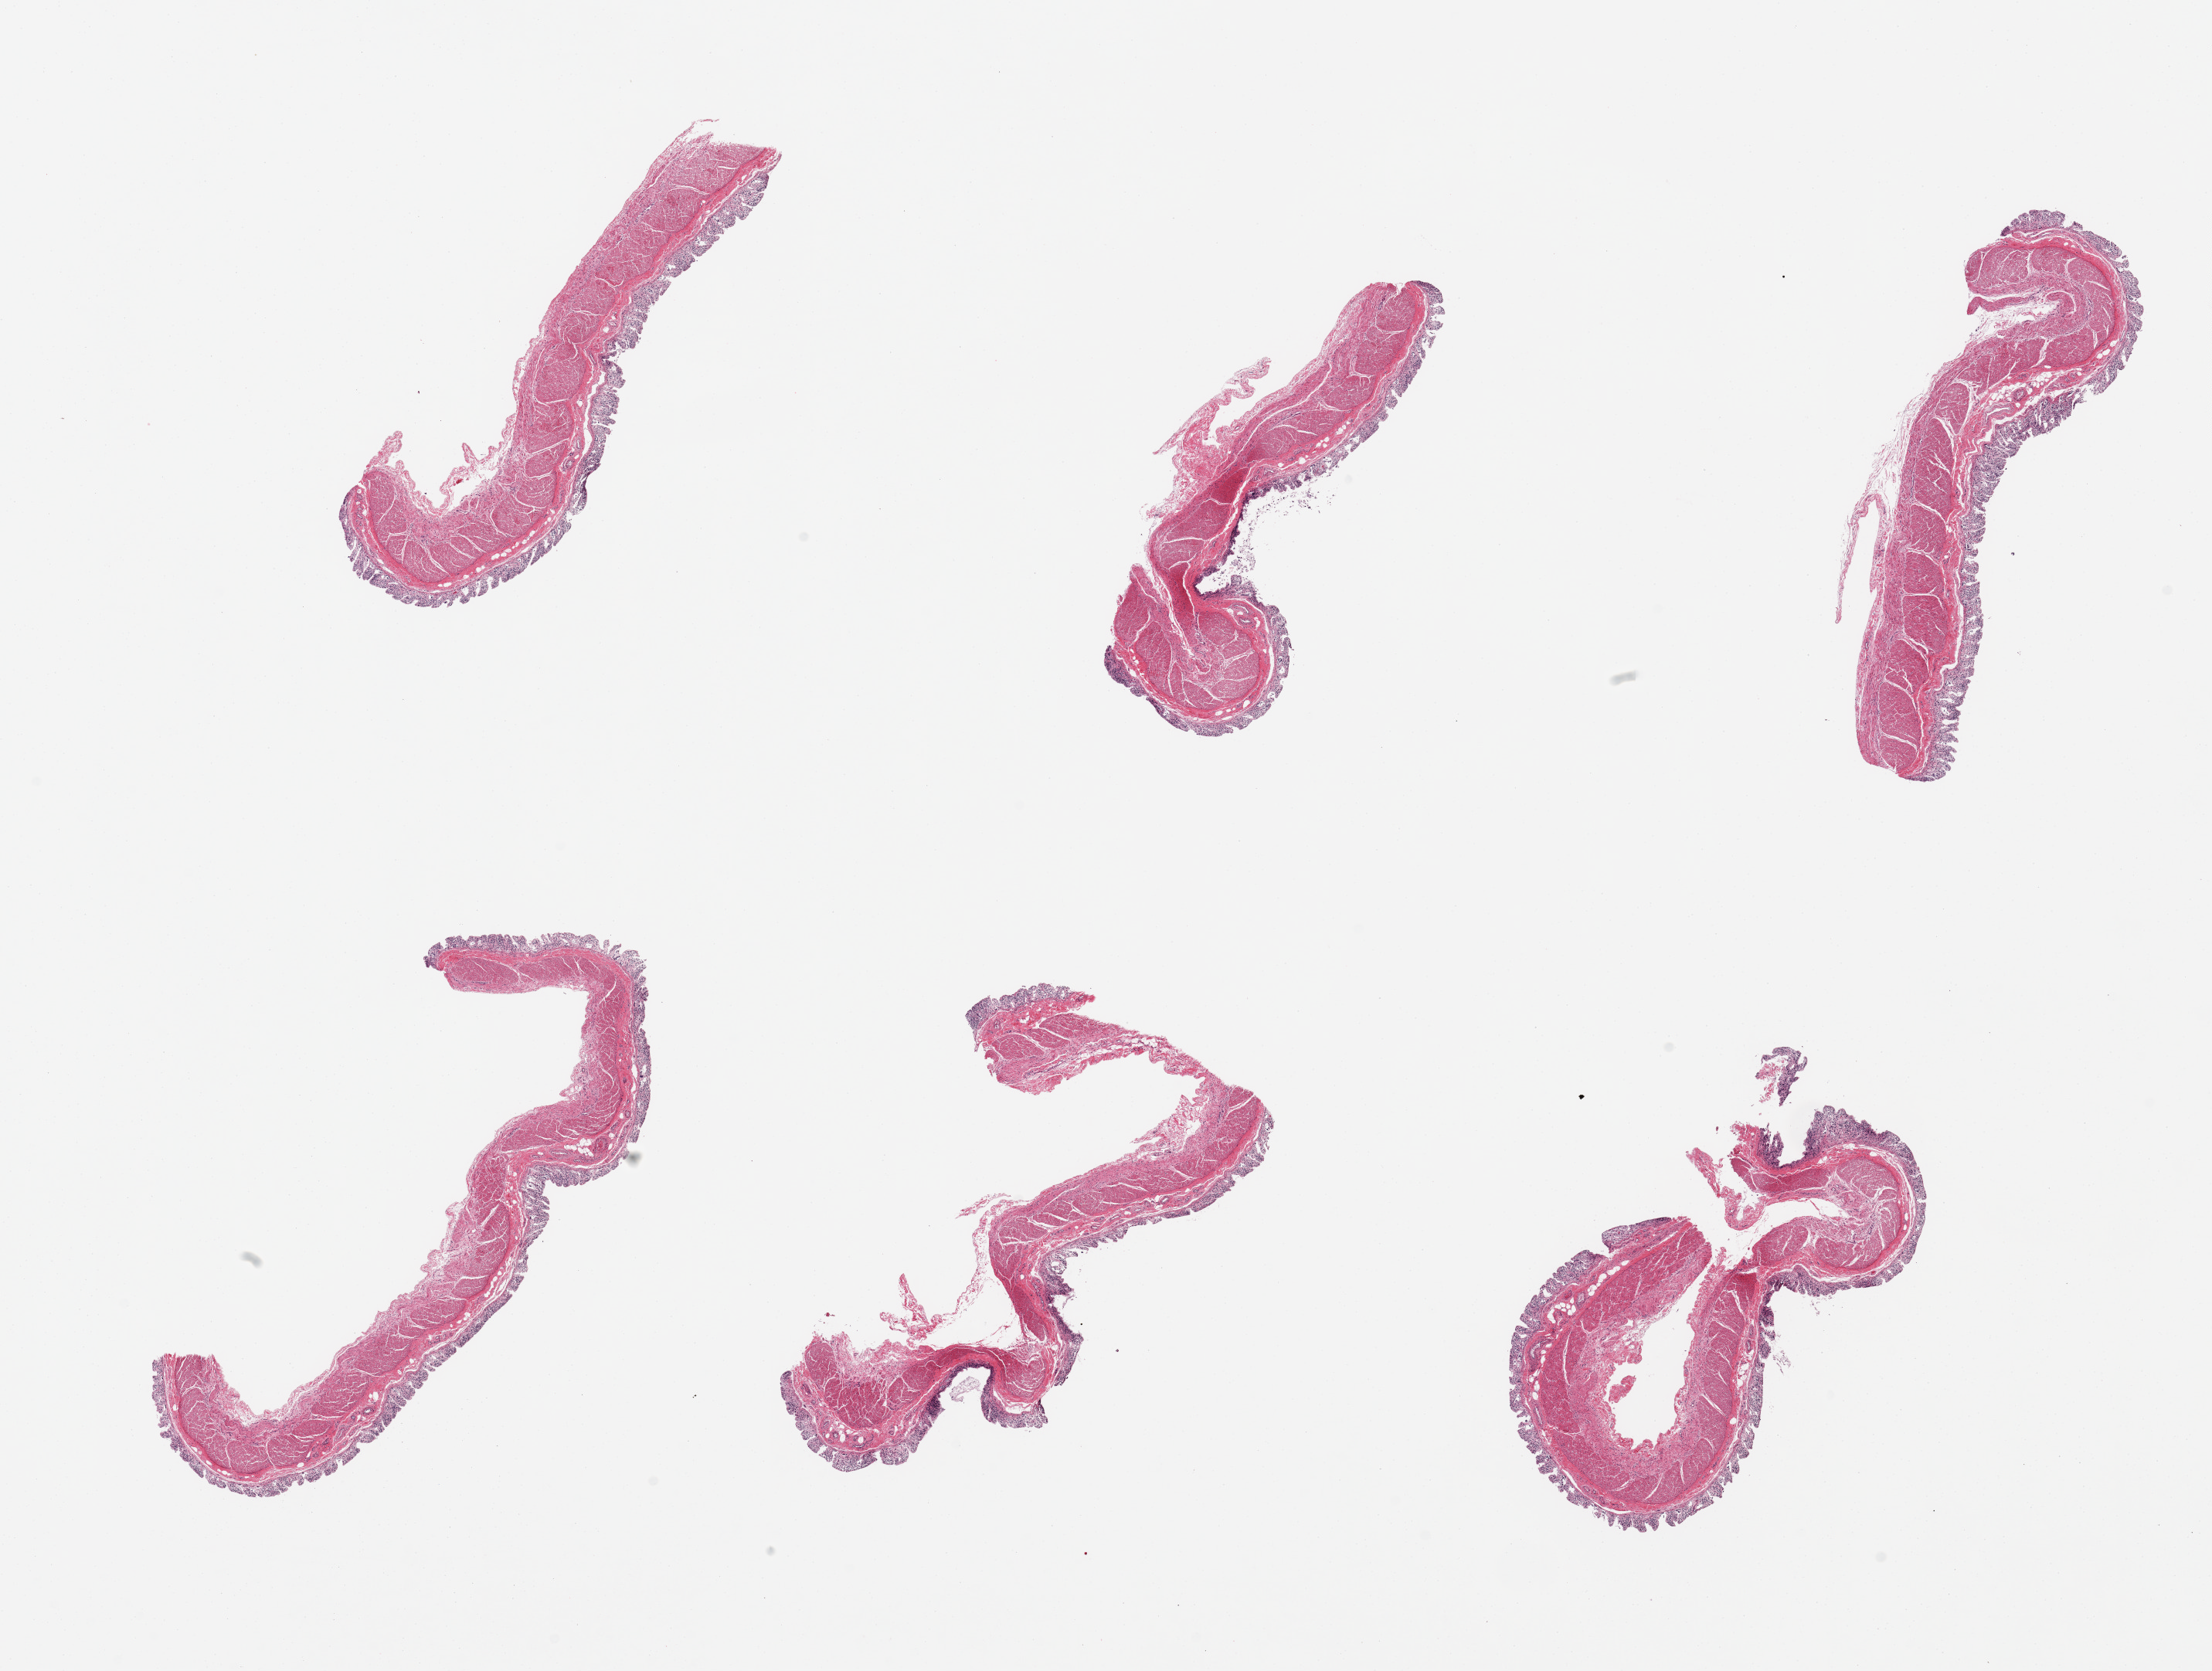
Whole-slide image, haematoxylin and eosin stain, low-resolution overview of the scanned area, about 22.6 x 17.1 mm (acquisition: 20x scan). PAXgene-fixed, paraffin-embedded tissue. Sampled site (target tissue): transverse colon. Donor tissue sample. Donor: male.
Review note (as recorded): 6 pieces, mucosa completely autolyzed, where visible, ~0.3mm.